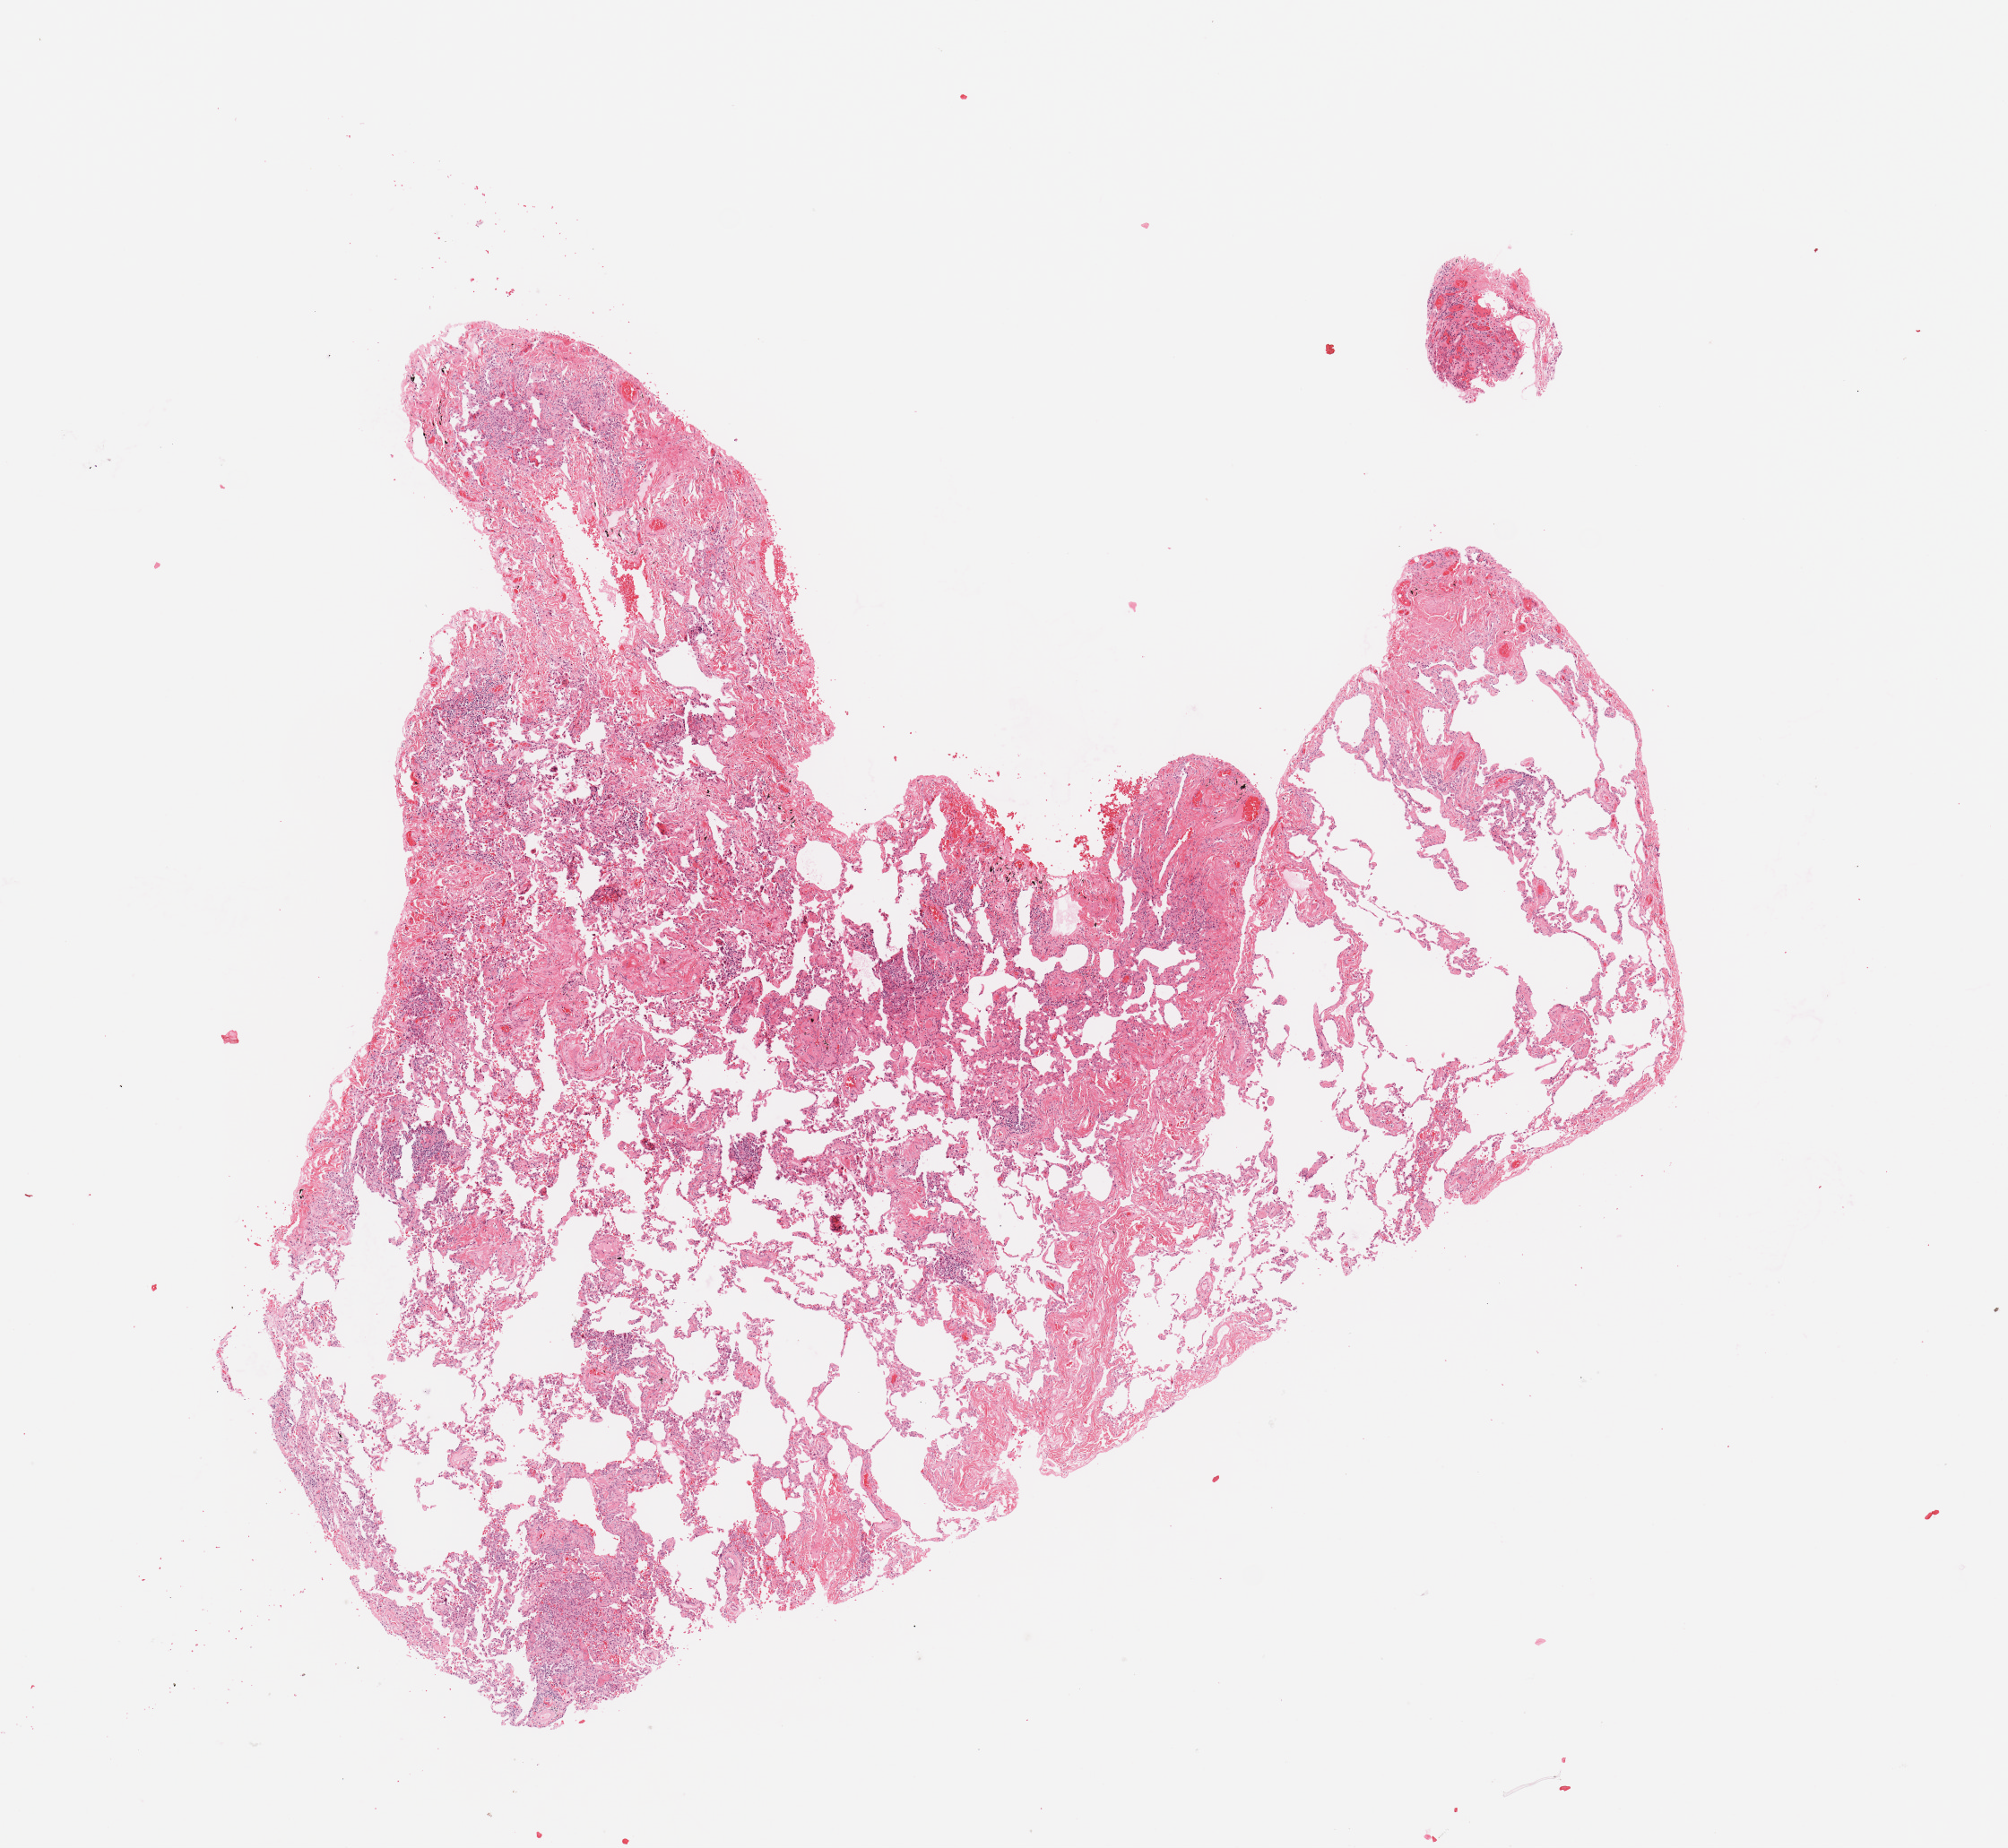
Digitized H&E-stained tissue section (whole slide), whole scanned area (about 8.9 x 8.2 mm) shown as a low-resolution overview, normal (non-tumour) tissue sample, sampled site: lung. 70-year-old female patient.
This section: normal (non-tumour) tissue from the same patient. Patient diagnosis: Adenocarcinoma, NOS.